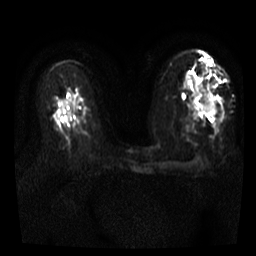
Breast MRI, one axial slice; position 16 of 35 along the scan axis; diffusion-weighted series; image 2 of 4 stored at this slice position (different b-values; order by instance number); 3 T; 256 × 256 image matrix, field of view 300 × 300 mm. Female patient.
Annotated regions visible in this slice (manually delineated by an expert):
- tumour on diffusion-weighted imaging: bounding box (x1, y1, x2, y2) in pixels: (201, 103, 216, 115)